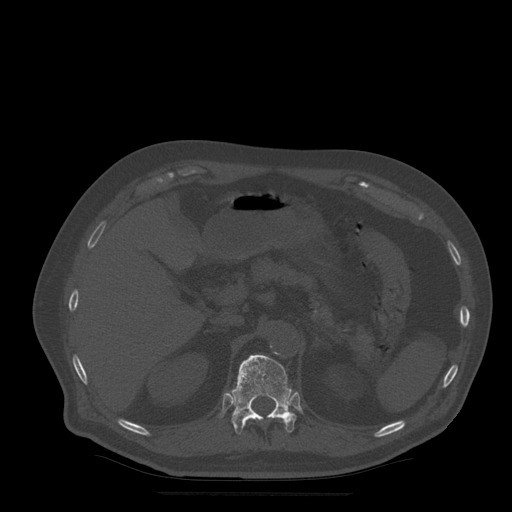
CT including the spine, one axial slice. Position 225 of 522 along the scan axis. Bone window (W 1800 / L 400 HU). 1.25 mm slice thickness. 512 × 512 image matrix, field of view 420 × 420 mm. Patient age 72 years. From the clinical record (not read from this slice): primary cancer: prostate.
Outlined on this slice (semi-automatically segmented with operator editing):
- T12 vertebra: box from (x=232, y=355) to (x=296, y=435) px